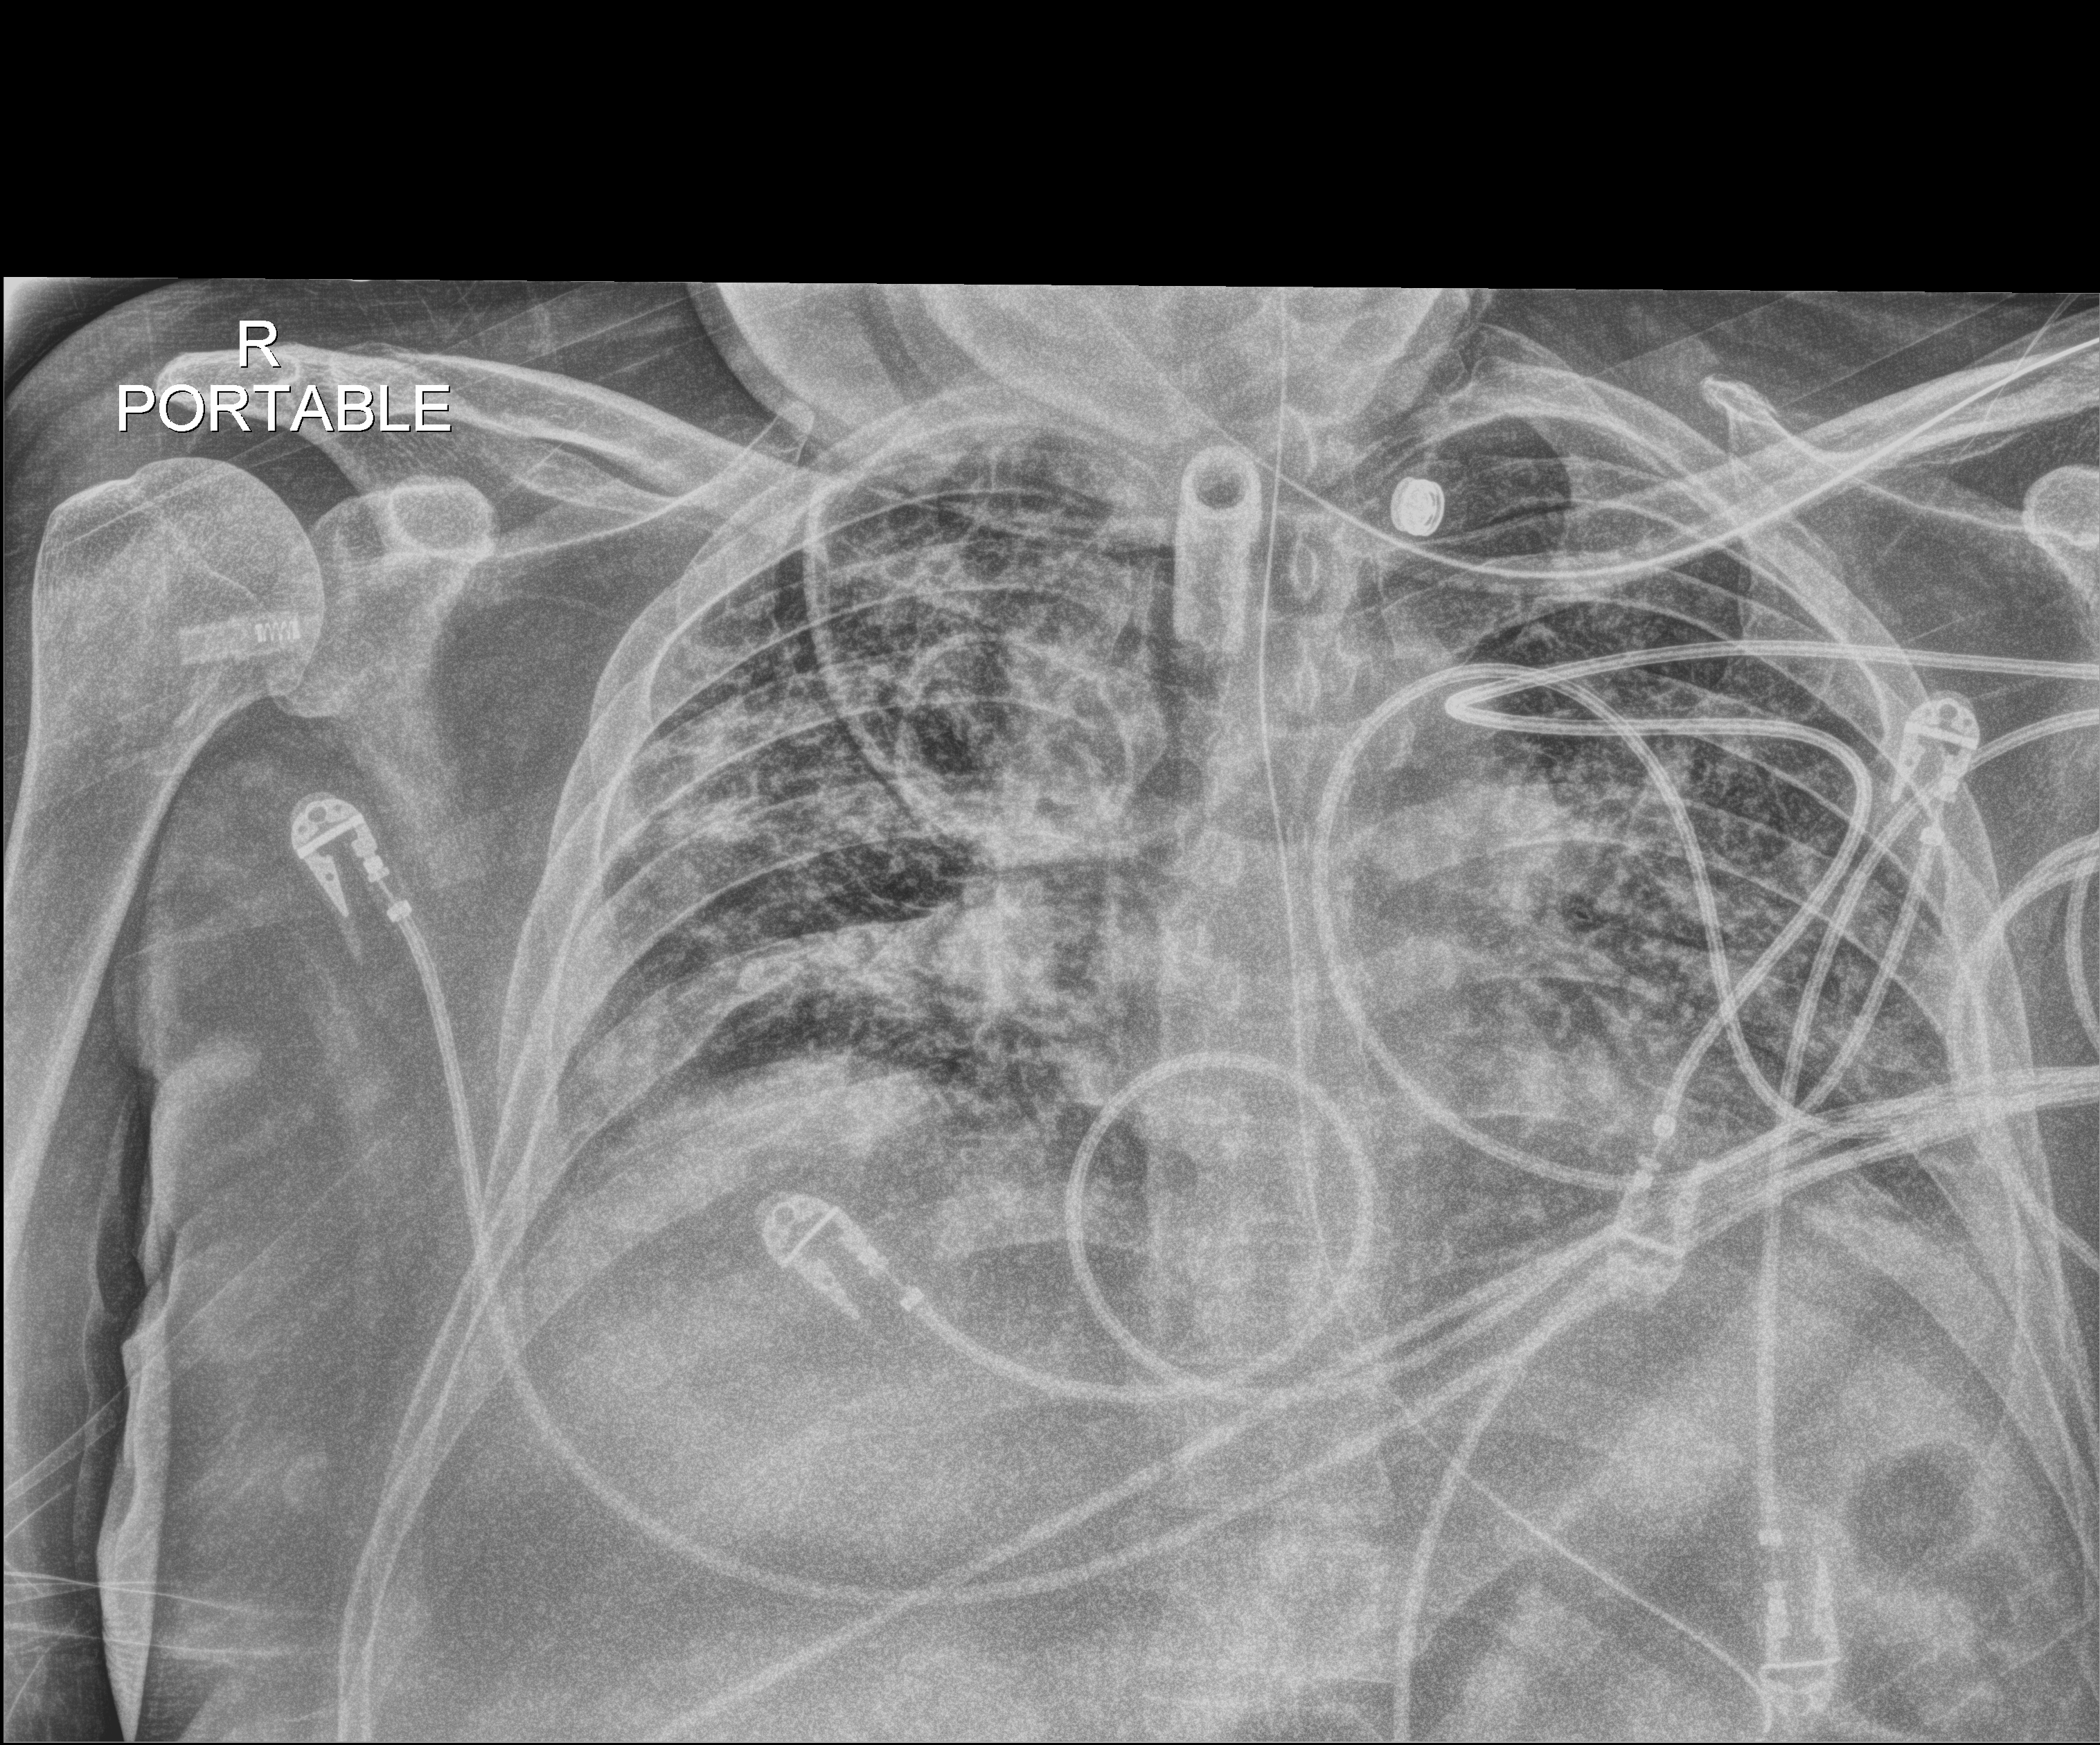
Portable chest radiograph; anteroposterior (AP) projection. Male patient hospitalised with COVID-19, age 18–59 years.
From the hospital-stay record, not from the radiograph (when in the stay this image was taken is not recorded): mechanically ventilated during this hospital stay: yes; admitted to intensive care during this hospital stay: yes; chronic kidney disease (admission record): no.